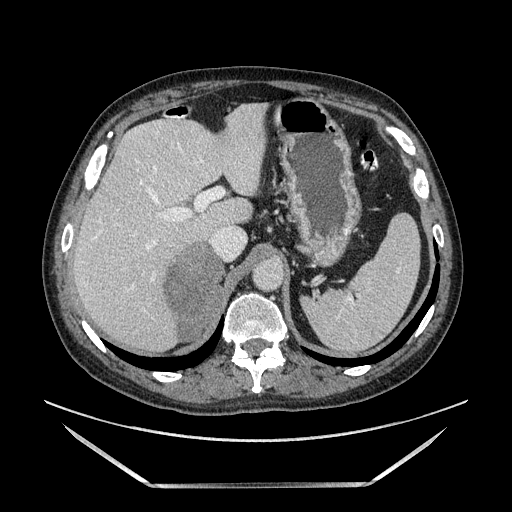
Contrast-enhanced abdominal CT, one axial slice; slice 104 of 185 in the series (ordered by position); soft-tissue window (W 400 / L 40 HU); 512 × 512 image matrix, field of view 440 × 440 mm. Male patient. From the clinical record (not read from this slice): diagnosis: adrenocortical carcinoma; tumour side: right adrenal; tumour size at pathology: 10.3 cm; Ki-67 index: 20 %; stage (as recorded): 3.
Structures marked on this image (semi-automatically segmented with operator editing):
- mass: bounding box <163,245,223,342> (left, top, right, bottom; pixels)